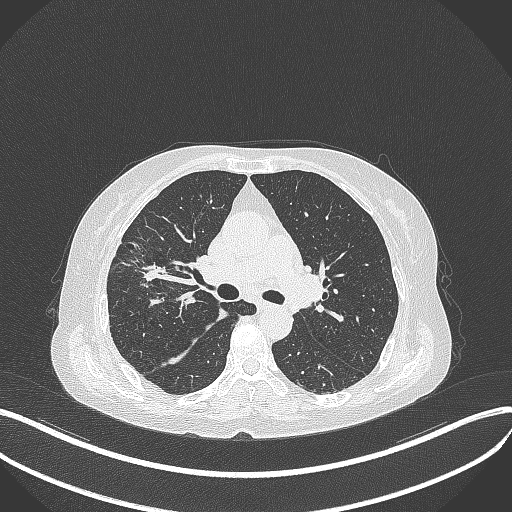
Chest CT, one axial slice. 120 kVp. Lung window (W 1500 / L -600 HU). 1 mm slice thickness. 512 × 512 image matrix. Female patient, age 69 years. Case-level facts recorded for this patient, not image findings: clinical TNM (as recorded): T1b N3 M0.
Structures marked on this image (bounding box drawn by a radiologist):
- lung tumour (recorded histology: small cell carcinoma): bounding box <130,259,176,286> (left, top, right, bottom; pixels)